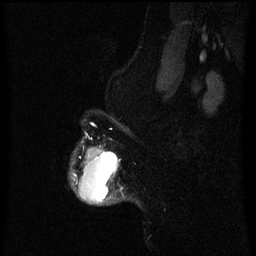
Breast MRI (dynamic contrast-enhanced), one sagittal slice. Position 55 of 60 along the scan axis. Dynamic contrast-enhanced series, image 2 of 3 at this slice position (ordered by acquisition). 1.5 T. TE 4.2 ms, TR 8 ms. 2 mm slice thickness. 256 × 256 image matrix, field of view 190 × 190 mm. Patient: female, 50 years.
Structures marked on this image (semi-automatic segmentation, software-assisted and operator-edited):
- analysis volume of interest (the breast-tissue region the enhancement analysis was run in; not a lesion): bounding box (x1, y1, x2, y2) in pixels: (70, 147, 119, 205)
- tumour enhancement mask (voxels above the 70 % enhancement threshold inside the analysis volume of interest): (73, 149, 116, 200)